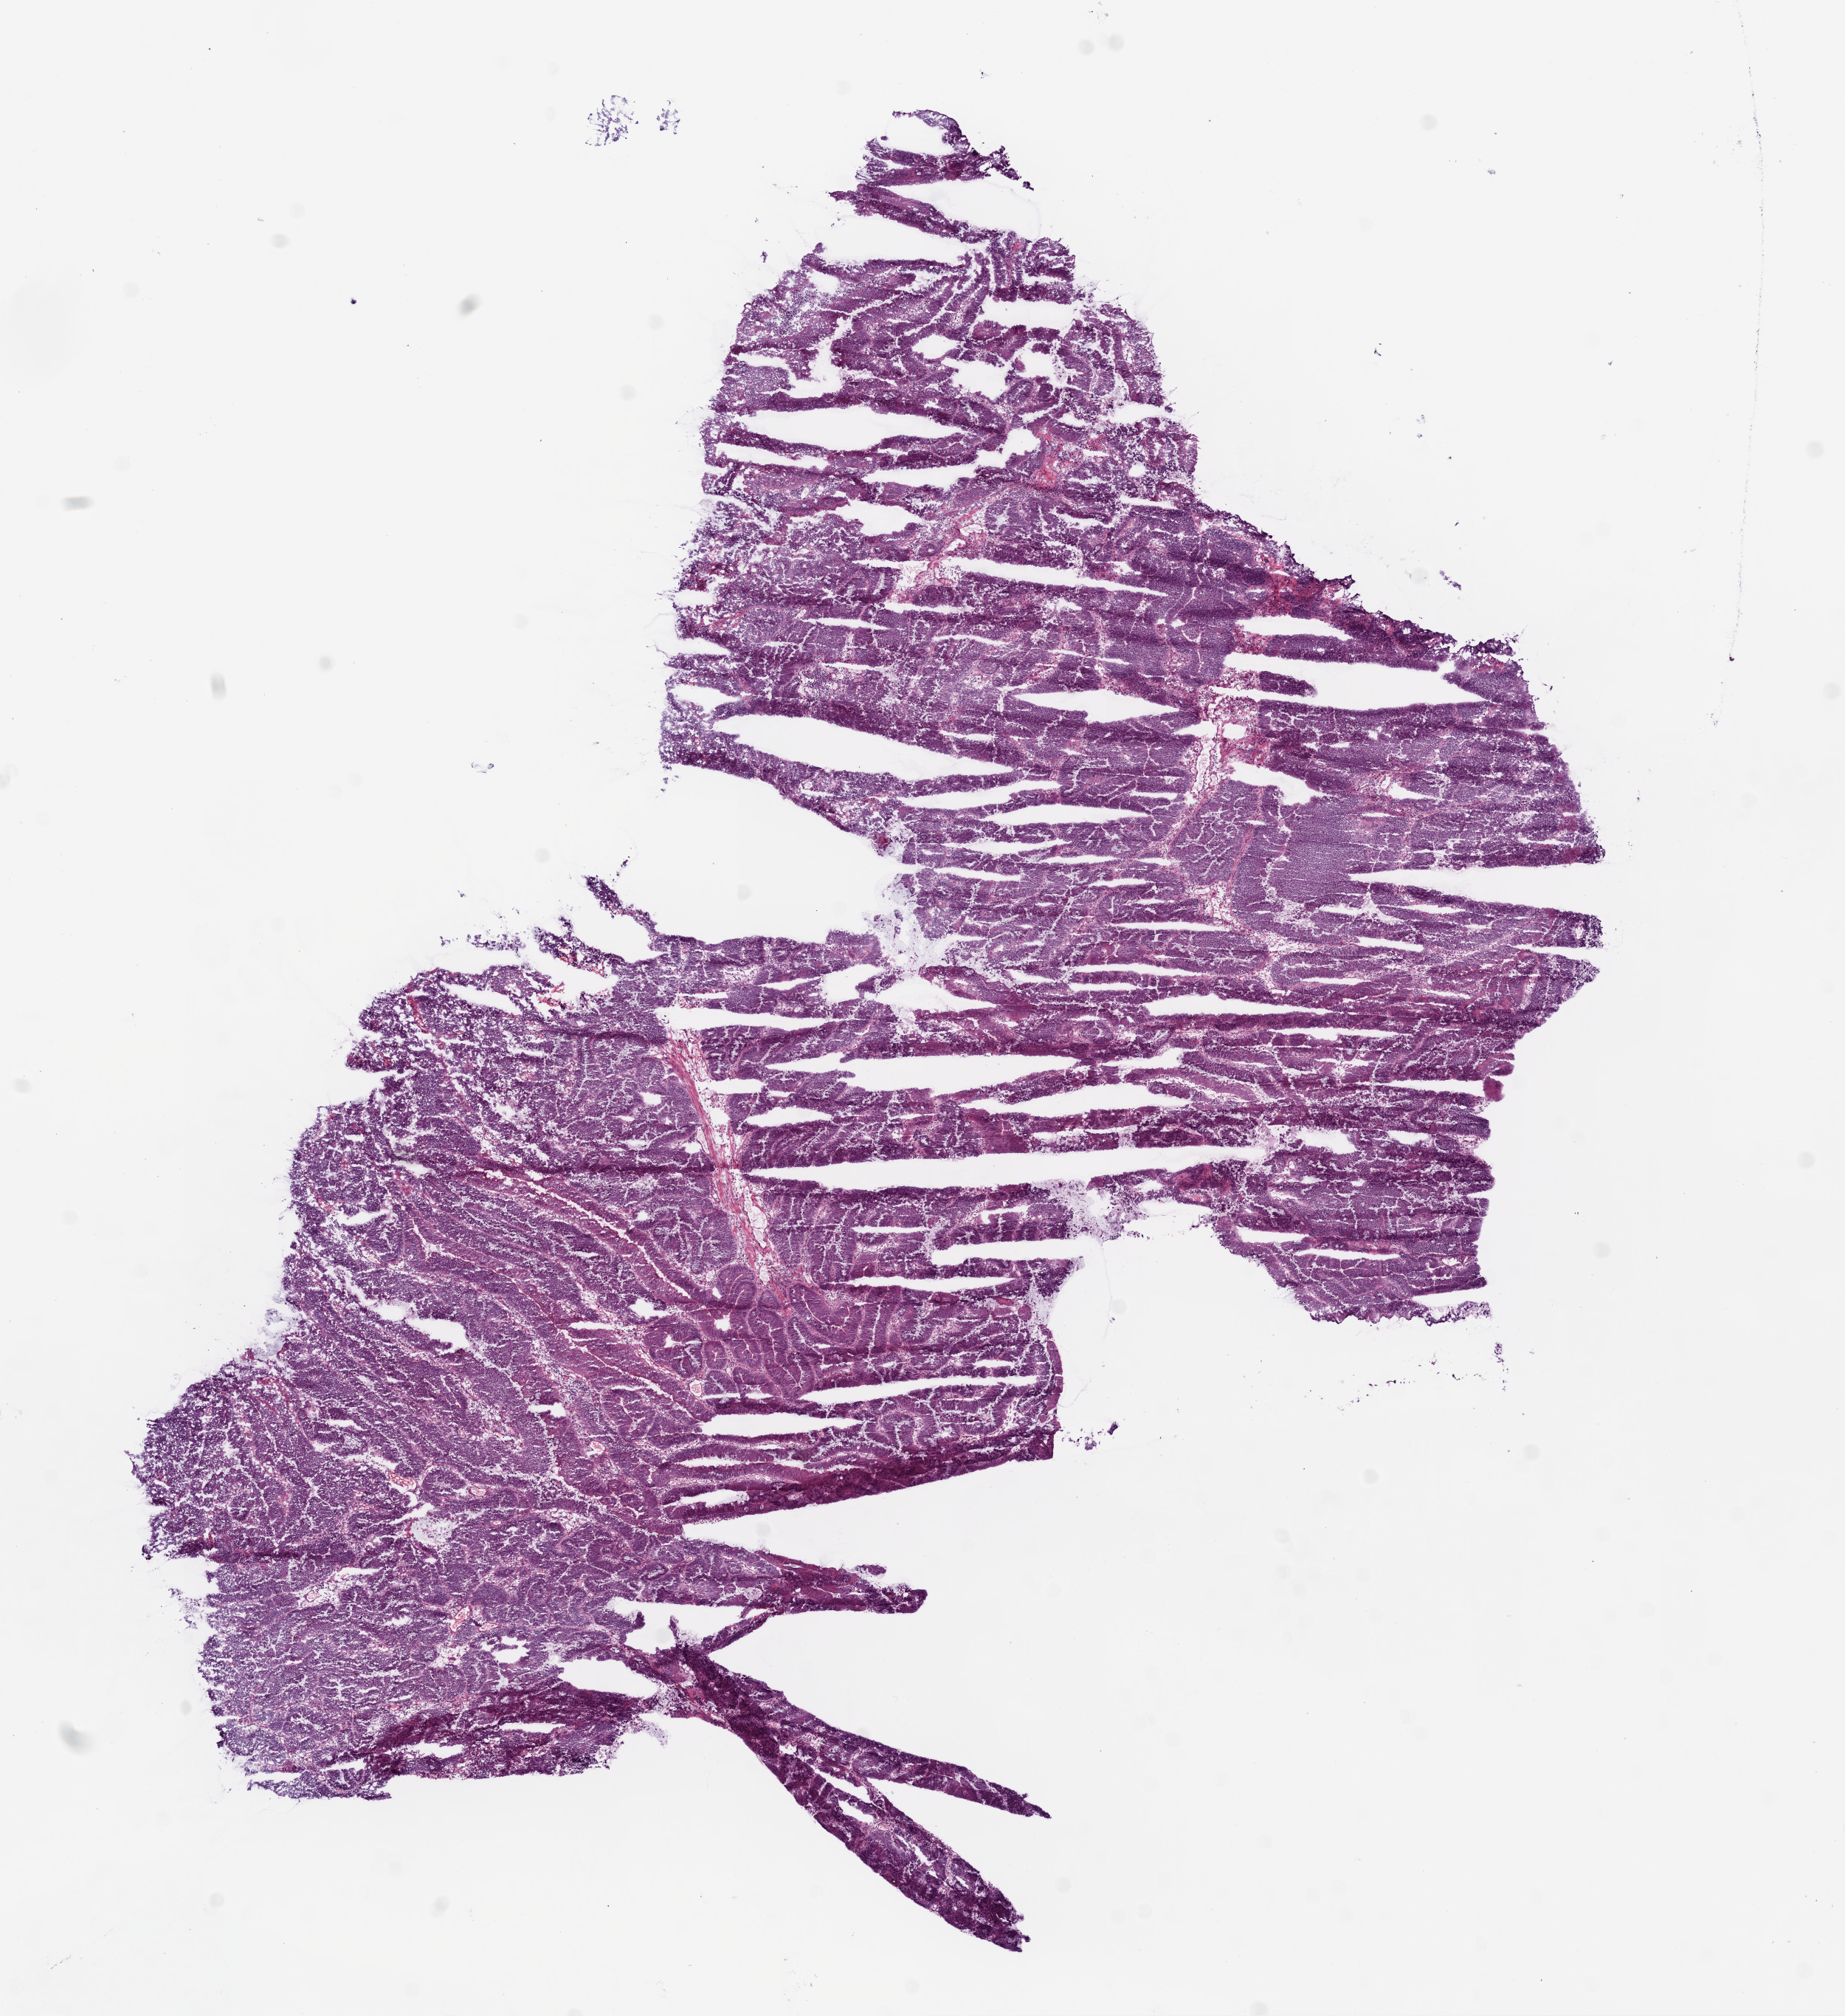
H&E whole-slide image, shown as a low-resolution overview of the whole scanned area (about 10.0 x 11.0 mm, slide scanned at 20x); frozen section; sample: primary tumour, rectum. Female patient; age at initial diagnosis 66 years. Slide review estimates, as recorded: tumour cells 92%, tumour nuclei 85%, normal cells 0%, stromal cells 5%, necrosis 3%.
TNM: T3 N0 M0. Diagnosis: Adenocarcinoma, NOS (rectosigmoid junction). AJCC pathologic stage: IIA (6th edition).